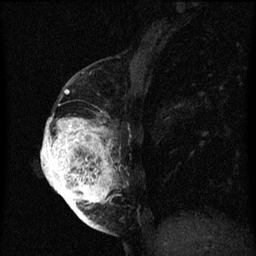
Breast MRI (dynamic contrast-enhanced), one sagittal slice. Dynamic contrast-enhanced series, image 2 of 3 at this slice position (ordered by acquisition). 1.5 T. TE 4.2 ms, TR 8 ms. 256 × 256 image matrix, field of view 180 × 180 mm. Female patient, age 56 years.
Annotated regions visible in this slice (semi-automatically segmented with operator editing):
- analysis volume of interest (the breast-tissue region the enhancement analysis was run in; not a lesion): bounding box [x1, y1, x2, y2] px = [42, 112, 123, 219]
- tumour enhancement mask (voxels above the 70 % enhancement threshold inside the analysis volume of interest): [42, 118, 115, 219]